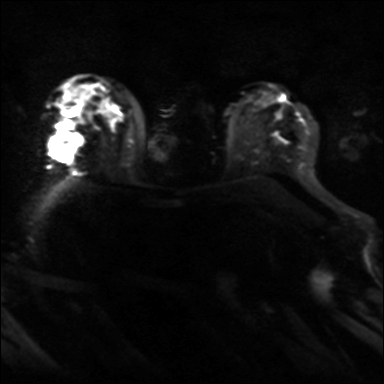
Breast MRI, one axial slice. Slice 23 of 36 in the series (ordered by position). Diffusion-weighted series; image 2 of 4 stored at this slice position (different b-values; order by instance number). 3 T. 4 mm slice thickness. 384 × 384 image matrix, field of view 320 × 320 mm. Female patient.
Structures marked on this image (expert manual segmentation):
- tumour on diffusion-weighted imaging: box from (x=50, y=131) to (x=81, y=160) px